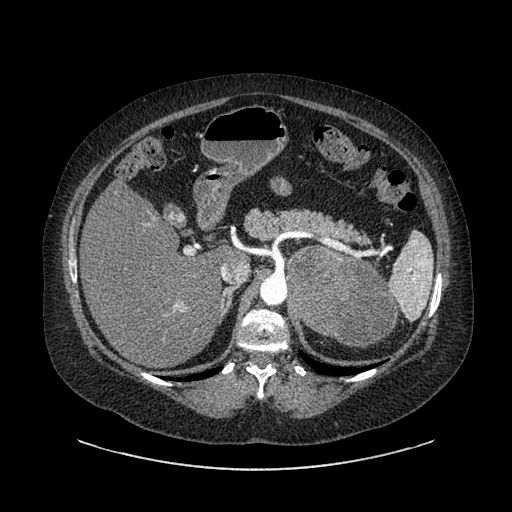
Contrast-enhanced abdominal CT, one axial slice. Slice 587 of 769 in the series (ordered by position). Intravenous contrast given. Soft-tissue window (W 400 / L 40 HU). 512 × 512 image matrix. Female patient, age 61 years. From the clinical record (not read from this slice): diagnosis: adrenocortical carcinoma; tumour side: left adrenal; tumour size at pathology: 13 cm; Ki-67 index: 79 %; stage (as recorded): 2.
Annotated regions visible in this slice (semi-automatic segmentation, software-assisted and operator-edited):
- mass: bounding box <287,249,396,345> (left, top, right, bottom; pixels)